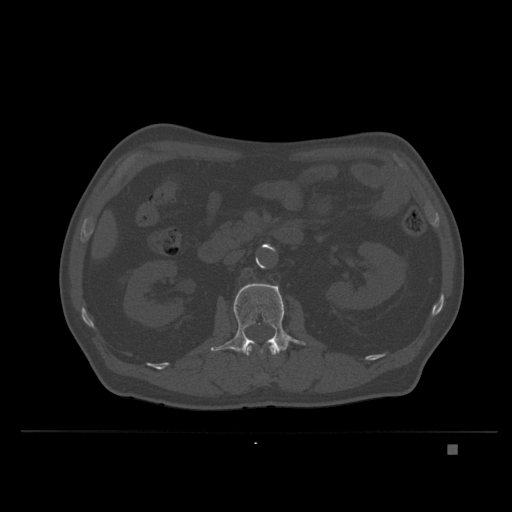
CT including the spine, one axial slice. Slice 121 of 435 in the series (ordered by position). Bone window (W 1800 / L 400 HU). 512 × 512 image matrix, field of view 434 × 434 mm. Male patient, age 73 years. From the clinical record (not read from this slice): primary cancer: skin.
Annotated regions visible in this slice (semi-automatic segmentation, software-assisted and operator-edited):
- L1 vertebra: bounding box [x1, y1, x2, y2] px = [246, 343, 277, 381]
- L2 vertebra: [211, 283, 305, 354]